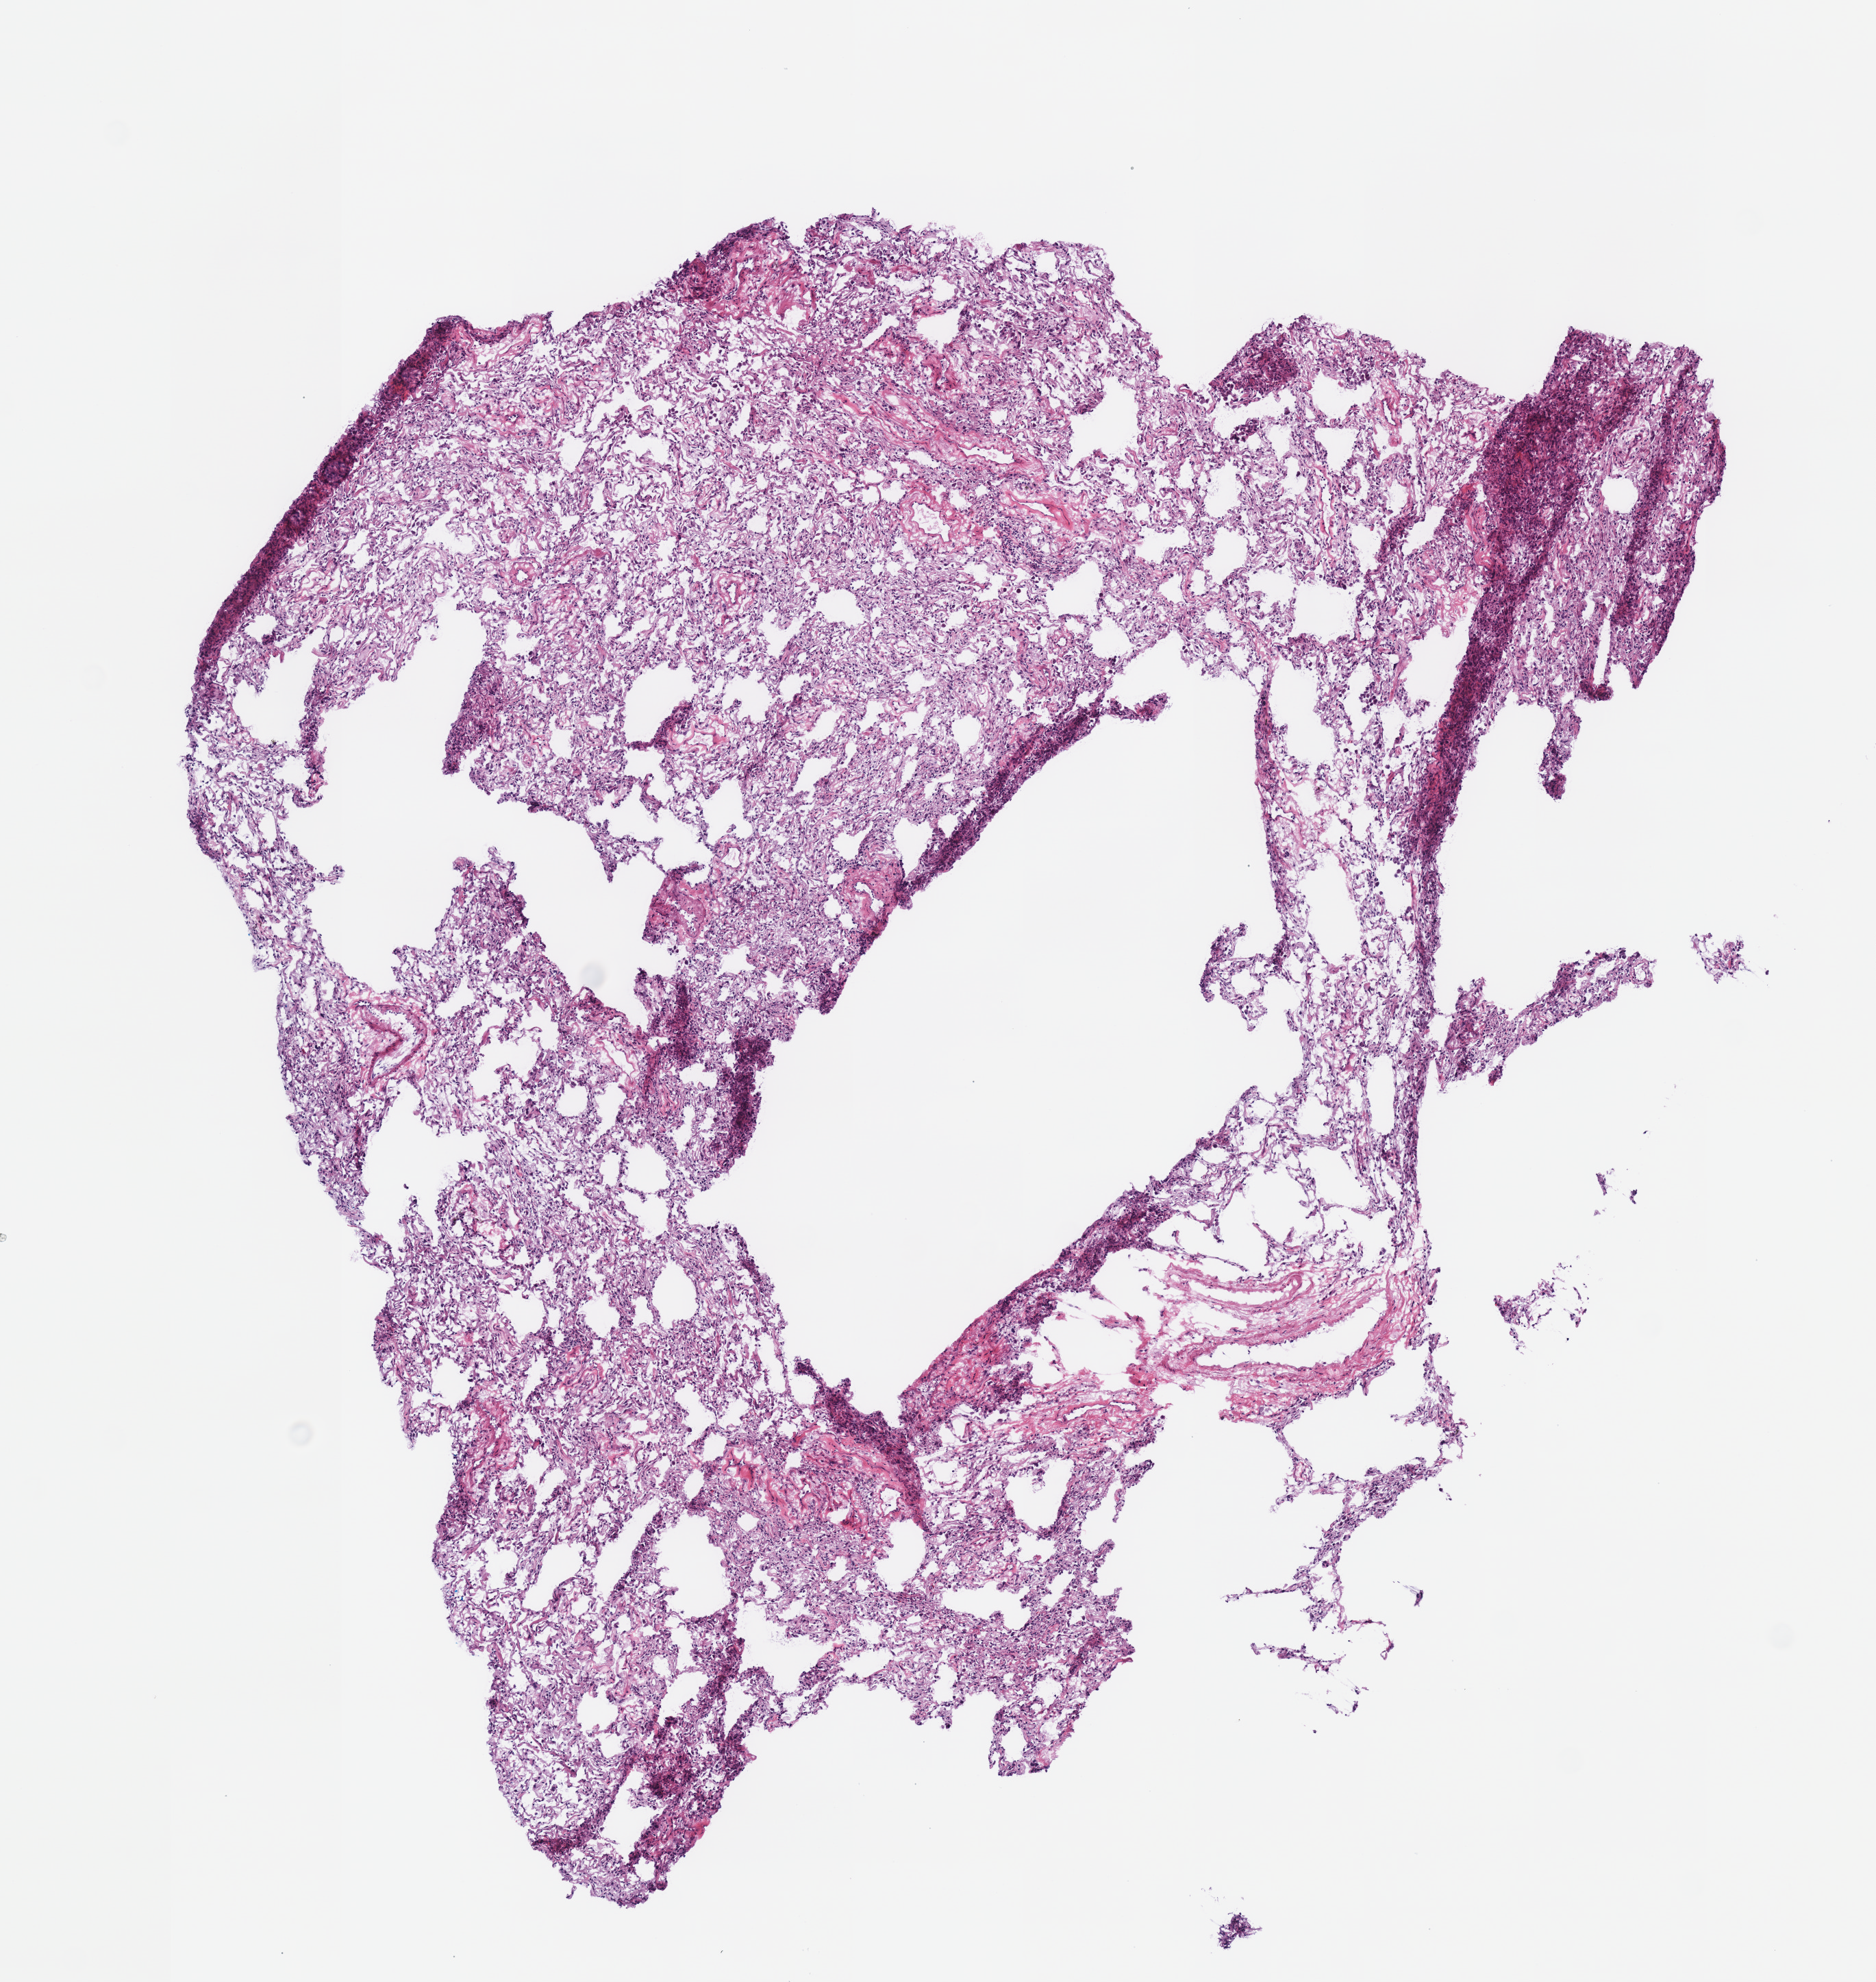
Whole-slide histology image, H&E, a low-resolution overview of the entire scanned area, about 5.4 x 5.7 mm, frozen section from the top of the tissue portion, solid tissue normal (non-tumour tissue) sample from the lung. Patient: female, age at initial diagnosis 72 years.
This section: solid tissue normal (non-tumour) sample from the same patient. Patient diagnosis: Mucinous adenocarcinoma (lower lobe, lung).